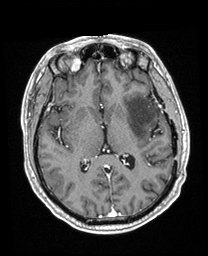
Brain MRI from a brain-tumour surgery series, one axial slice; slice 106 of 208 in the series (ordered by position); T1-weighted post-contrast; 1 mm slice thickness; 208 × 256 image matrix, field of view 211 × 260 mm. From the clinical record (not read from this slice): histopathology: Astrocytoma; WHO grade: 3; IDH mutation: yes.
Outlined on this slice (outlined manually by an expert reader):
- previous resection cavity: bounding box (x1, y1, x2, y2) in pixels: (150, 124, 162, 138)